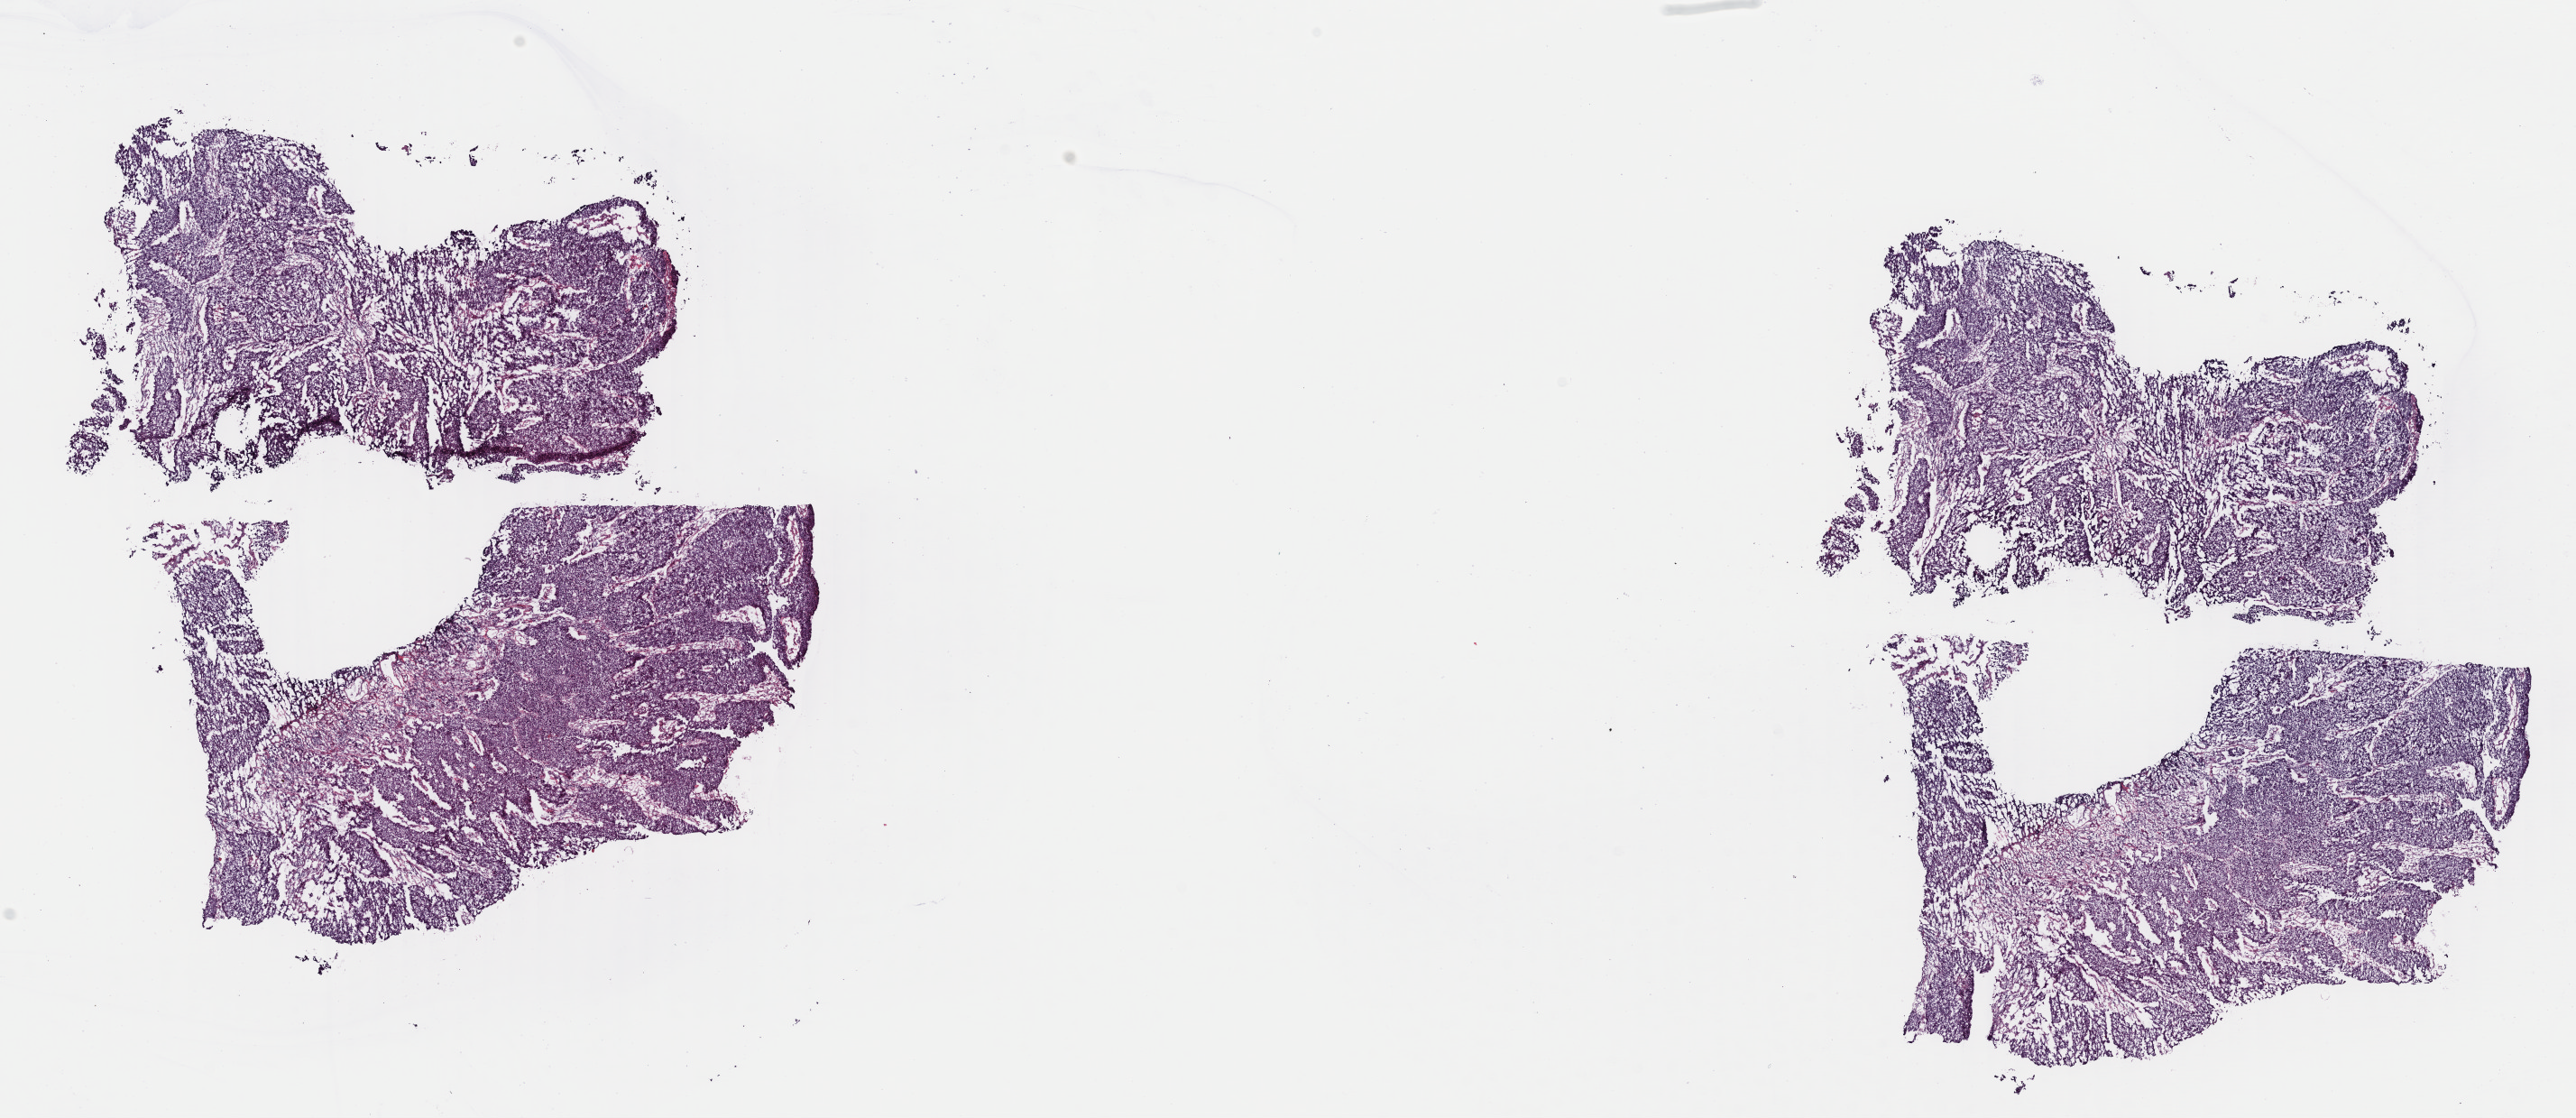
Digitized Hematoxylin and eosin (H&E) stained tissue section (whole slide), low-resolution overview of the scanned area, about 22.5 x 9.8 mm (acquisition: 40x scan), frozen section, sample: primary tumour, bladder. Male, age 71 years at initial diagnosis. Histologic grade: high grade. Slide review estimates, as recorded: tumour cells 85%, tumour nuclei 90%, normal cells 0%, stromal cells 15%, necrosis 0%. Inflammatory infiltration, as recorded: lymphocyte infiltration 0%, monocyte infiltration 0%, neutrophil infiltration 0%.
AJCC pathologic stage: III (7th edition). Lymph nodes positive (case pathology): 0 of 5 examined. Histologic diagnosis: Transitional cell carcinoma.